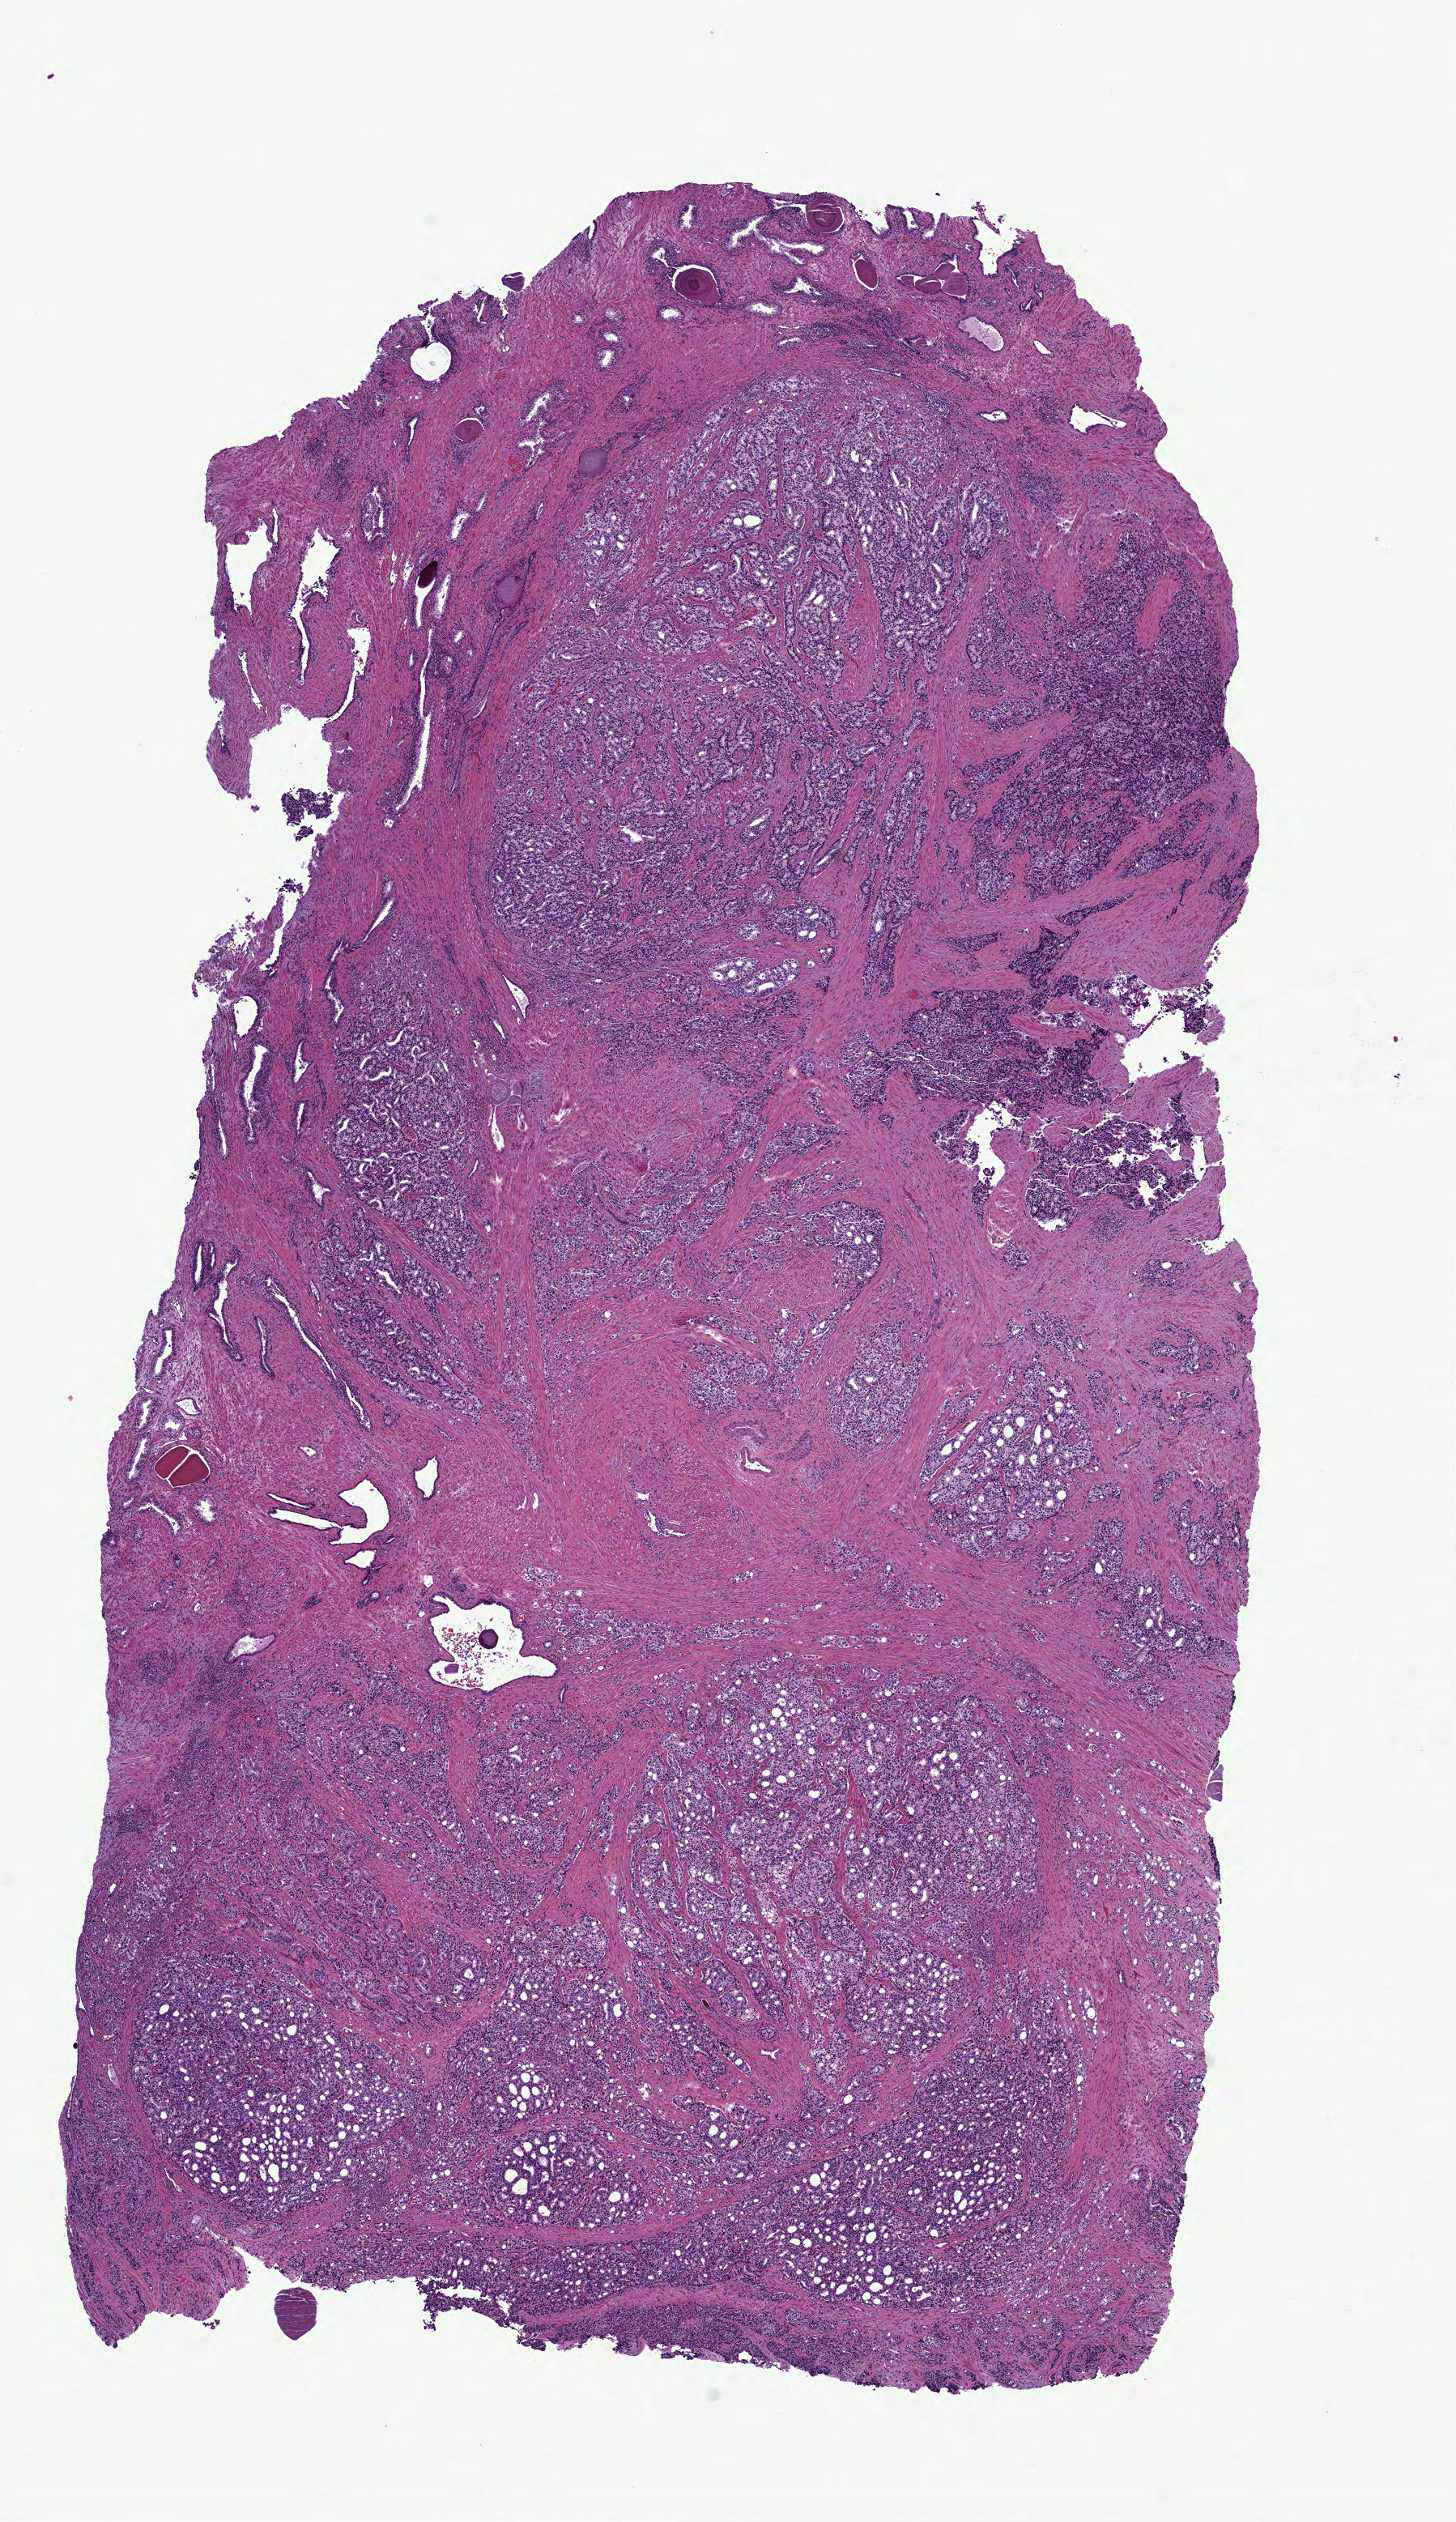
Digitized H&E-stained tissue section (whole slide) — low-resolution overview of the scanned area, about 7.3 x 12.6 mm (acquisition: 40x scan). Formalin-fixed paraffin-embedded (FFPE) diagnostic section. Primary tumour sample from the prostate. Male patient; age at initial diagnosis 63 years. Gleason score: 9 (5+4).
- pathologic diagnosis: Adenocarcinoma, NOS (prostate gland)